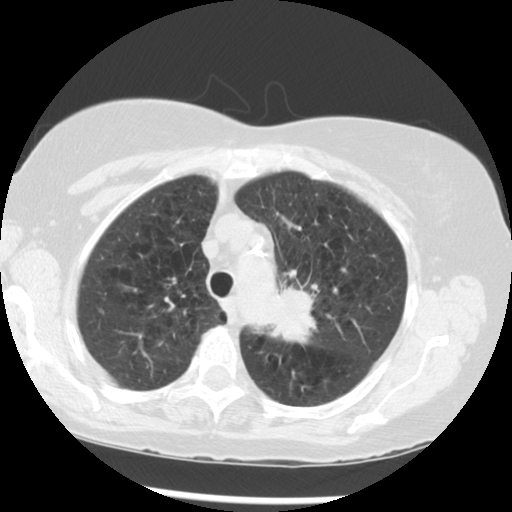
Low-dose screening chest CT, one axial slice. Slice 219 of 283 in the series (ordered by position). Reconstruction kernel STANDARD. 120 kVp. Lung window (W 1500 / L -600 HU). 512 × 512 image matrix, field of view 330 × 330 mm.
Structures marked on this image (manually delineated by an expert):
- lesion 1 (tumor, upper lobe of left lung): box from (x=270, y=288) to (x=315, y=343) px